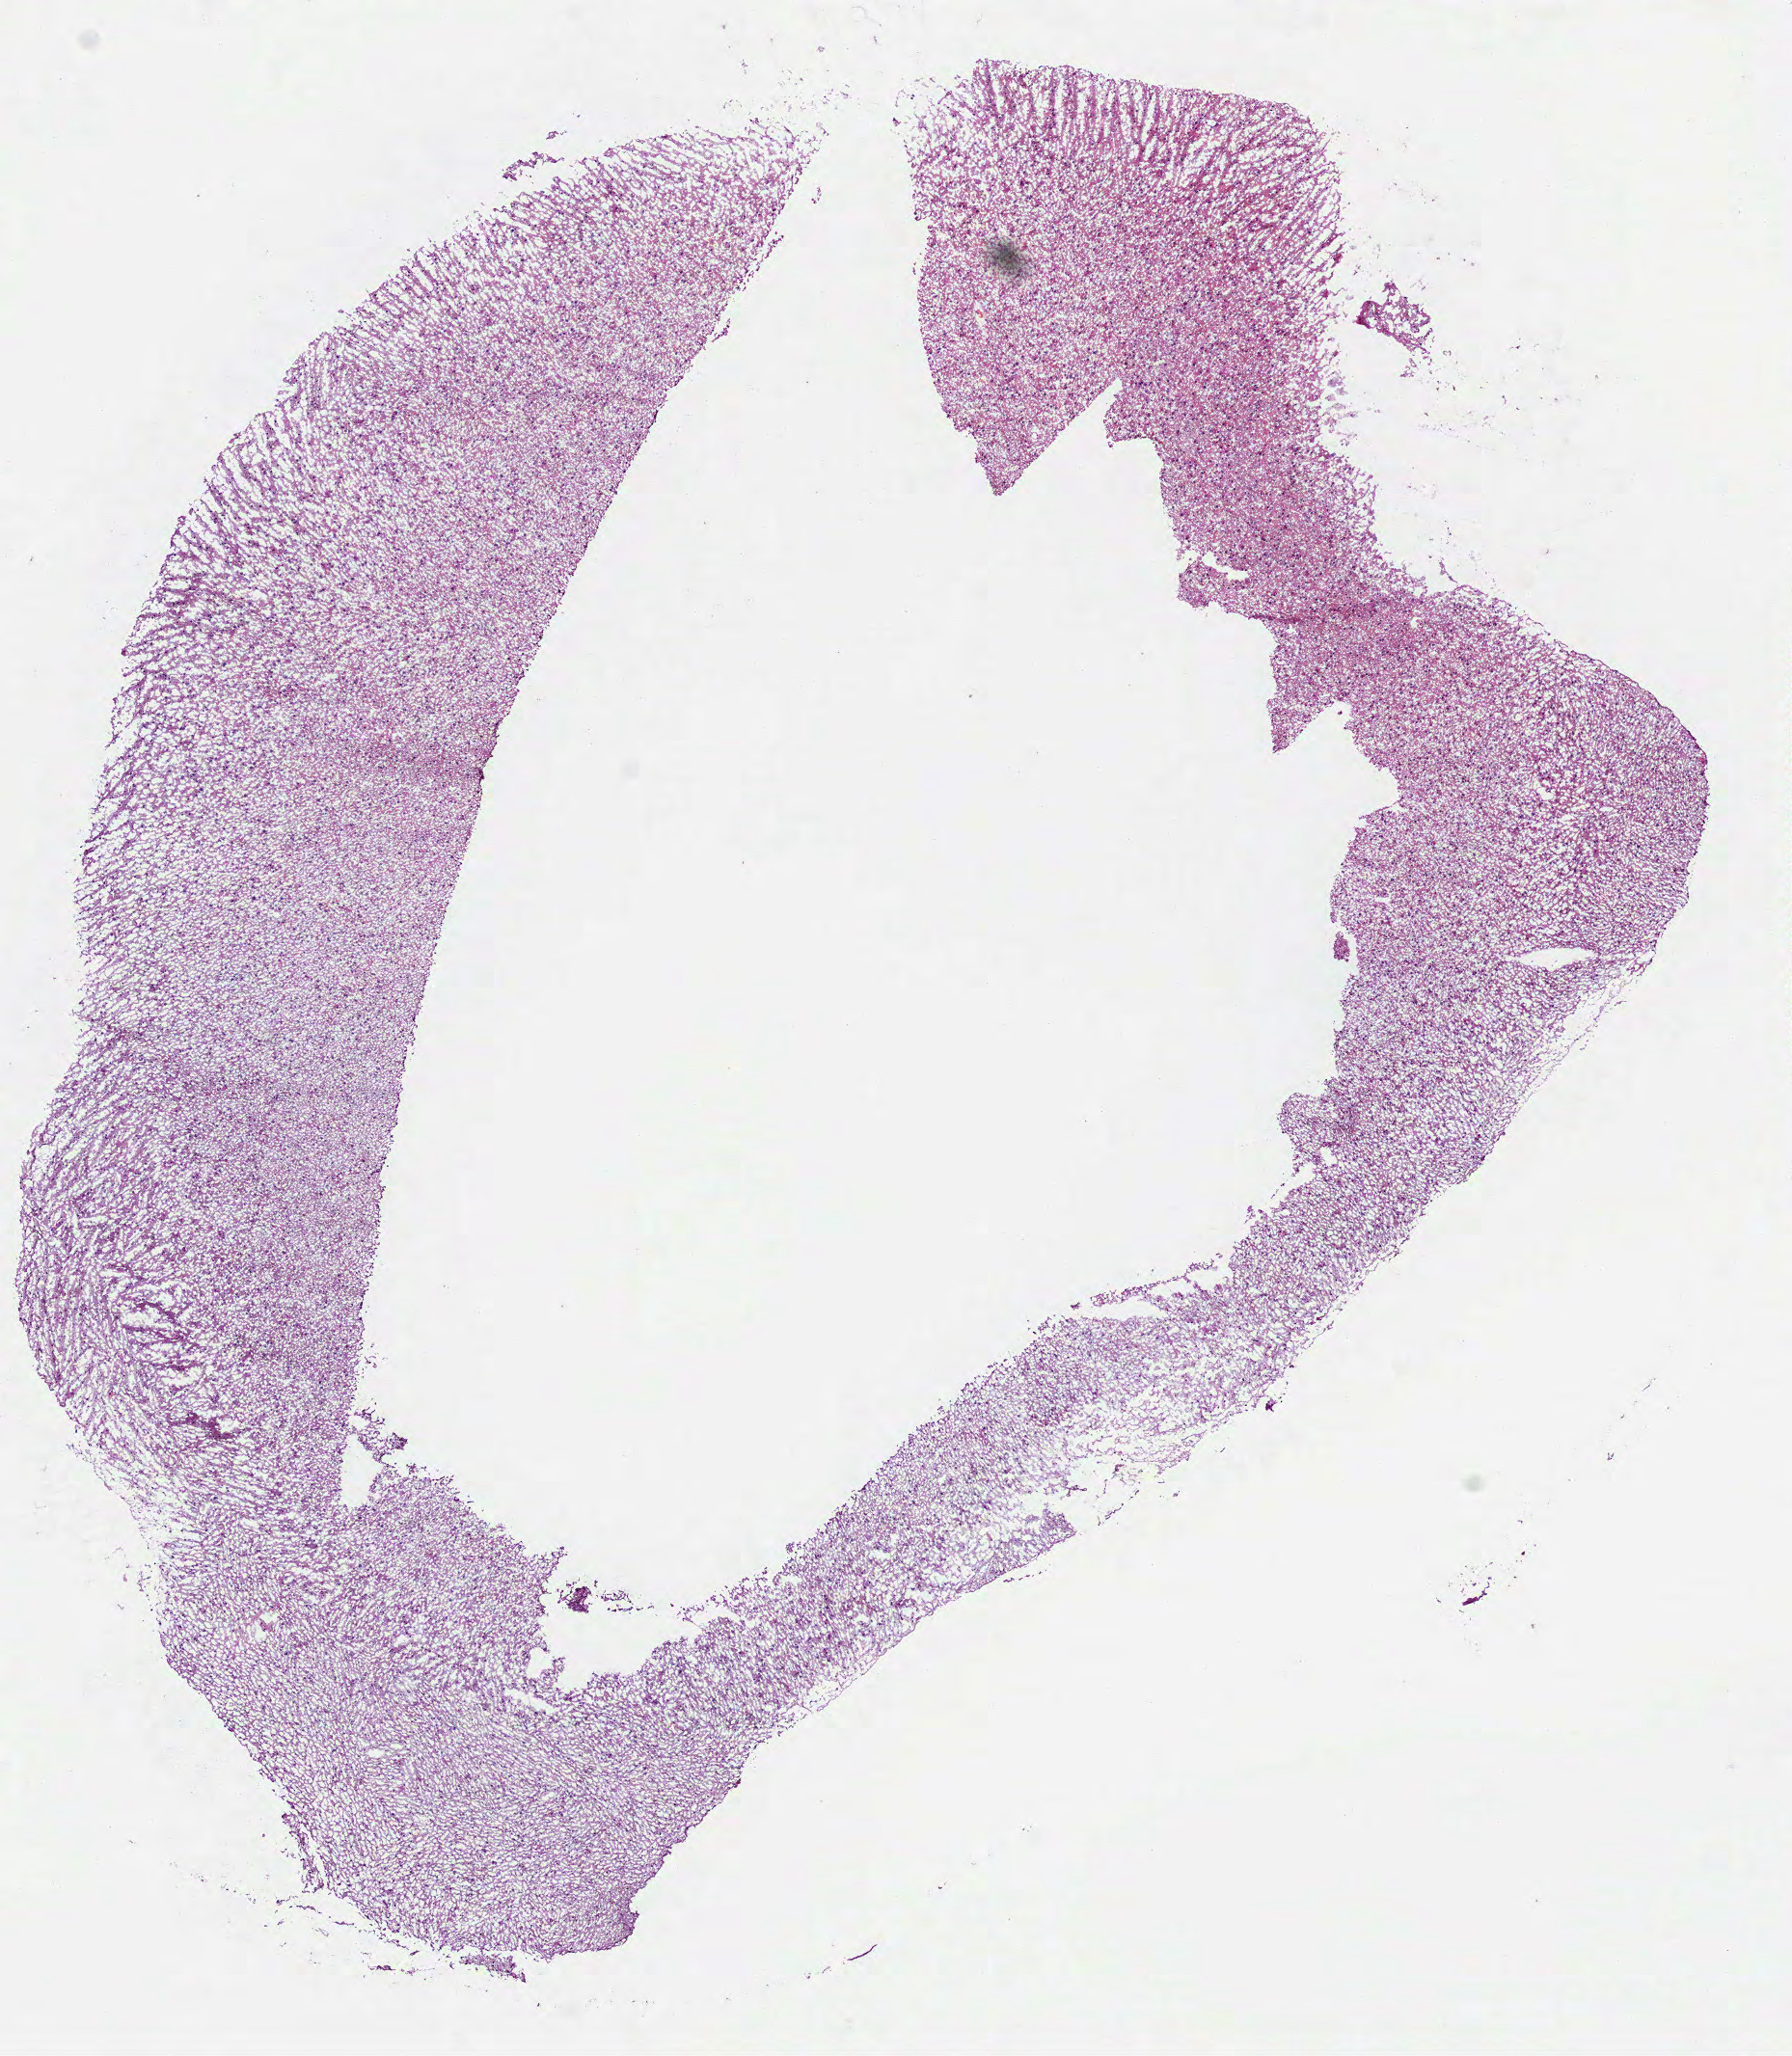
Digitized Hematoxylin and eosin (H&E) stained tissue section (whole slide), shown as a low-resolution overview of the whole scanned area (about 7.5 x 8.6 mm, slide scanned at 40x), frozen section from the bottom of the tissue portion, brain, primary tumour sample. Patient: male, age at initial diagnosis 42 years.
Diagnosis: Astrocytoma, NOS.